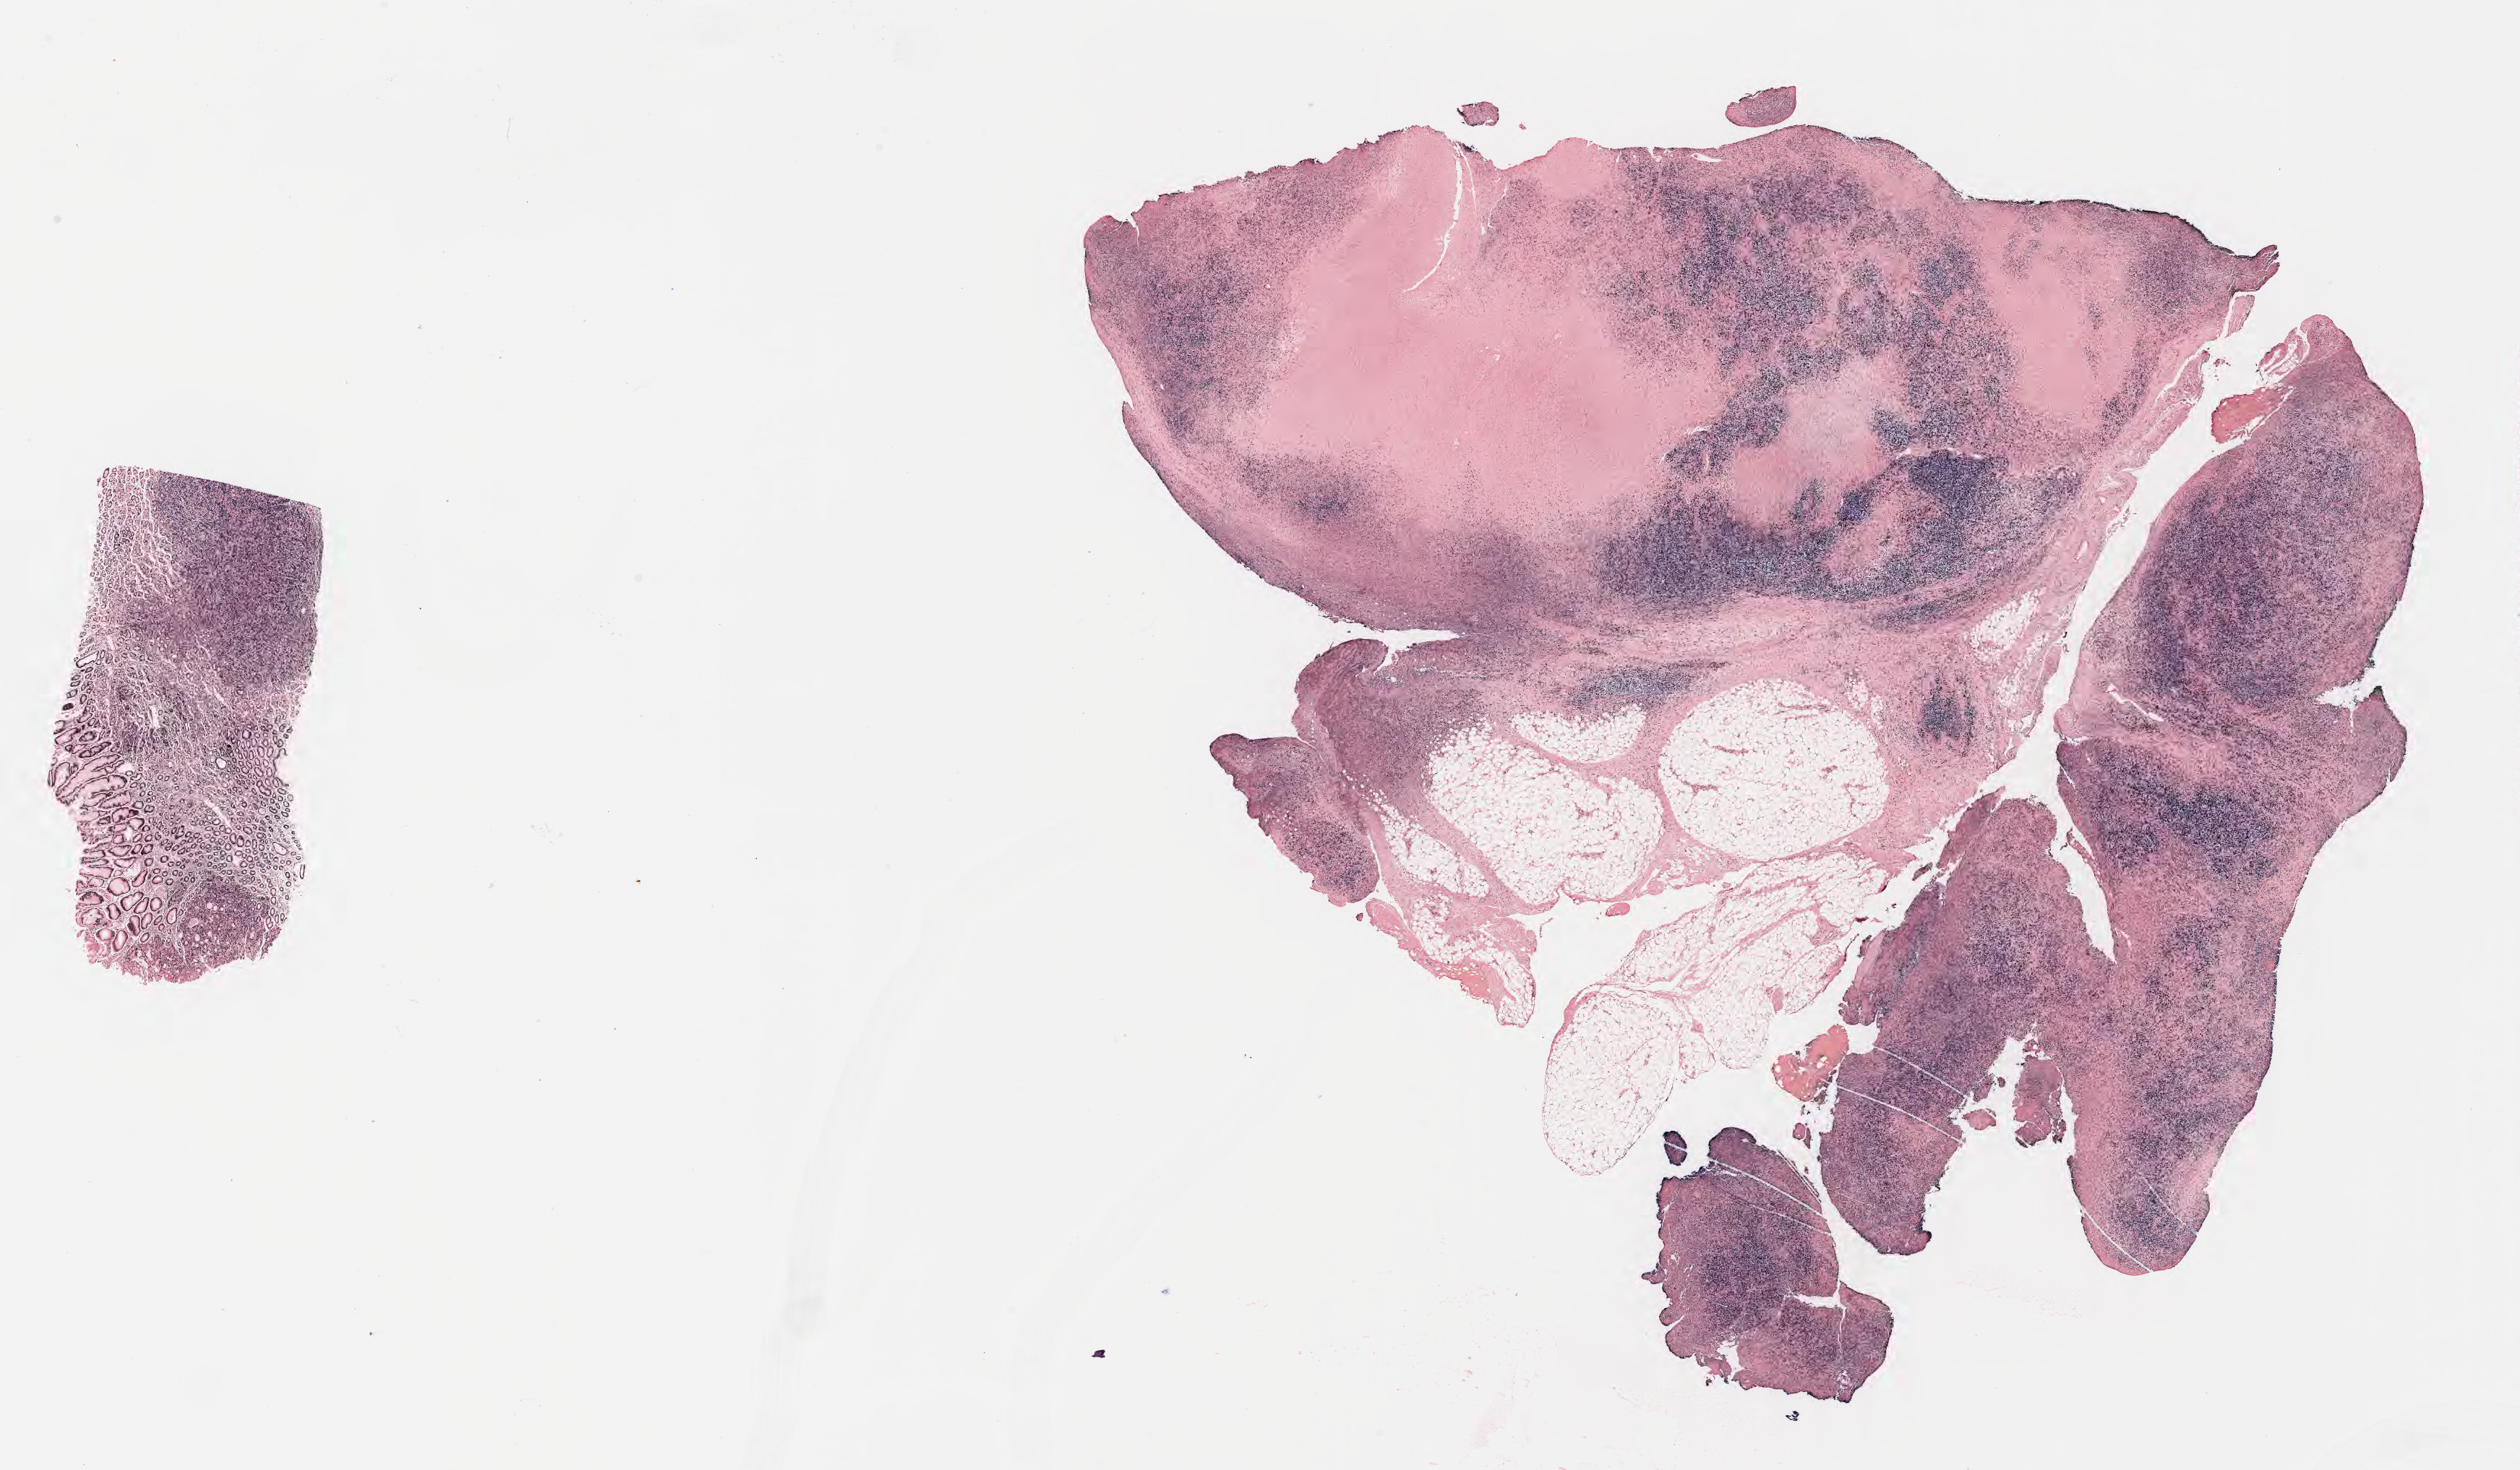
Whole-slide image; stain recorded as Iodonitrotetrazolium, whole scanned area (about 28.2 x 16.4 mm) shown as a low-resolution overview. Specimen: tumor tissue. Patient: female, 46 years old.
Histologic diagnosis: Diffuse large B-cell lymphoma, NOS.